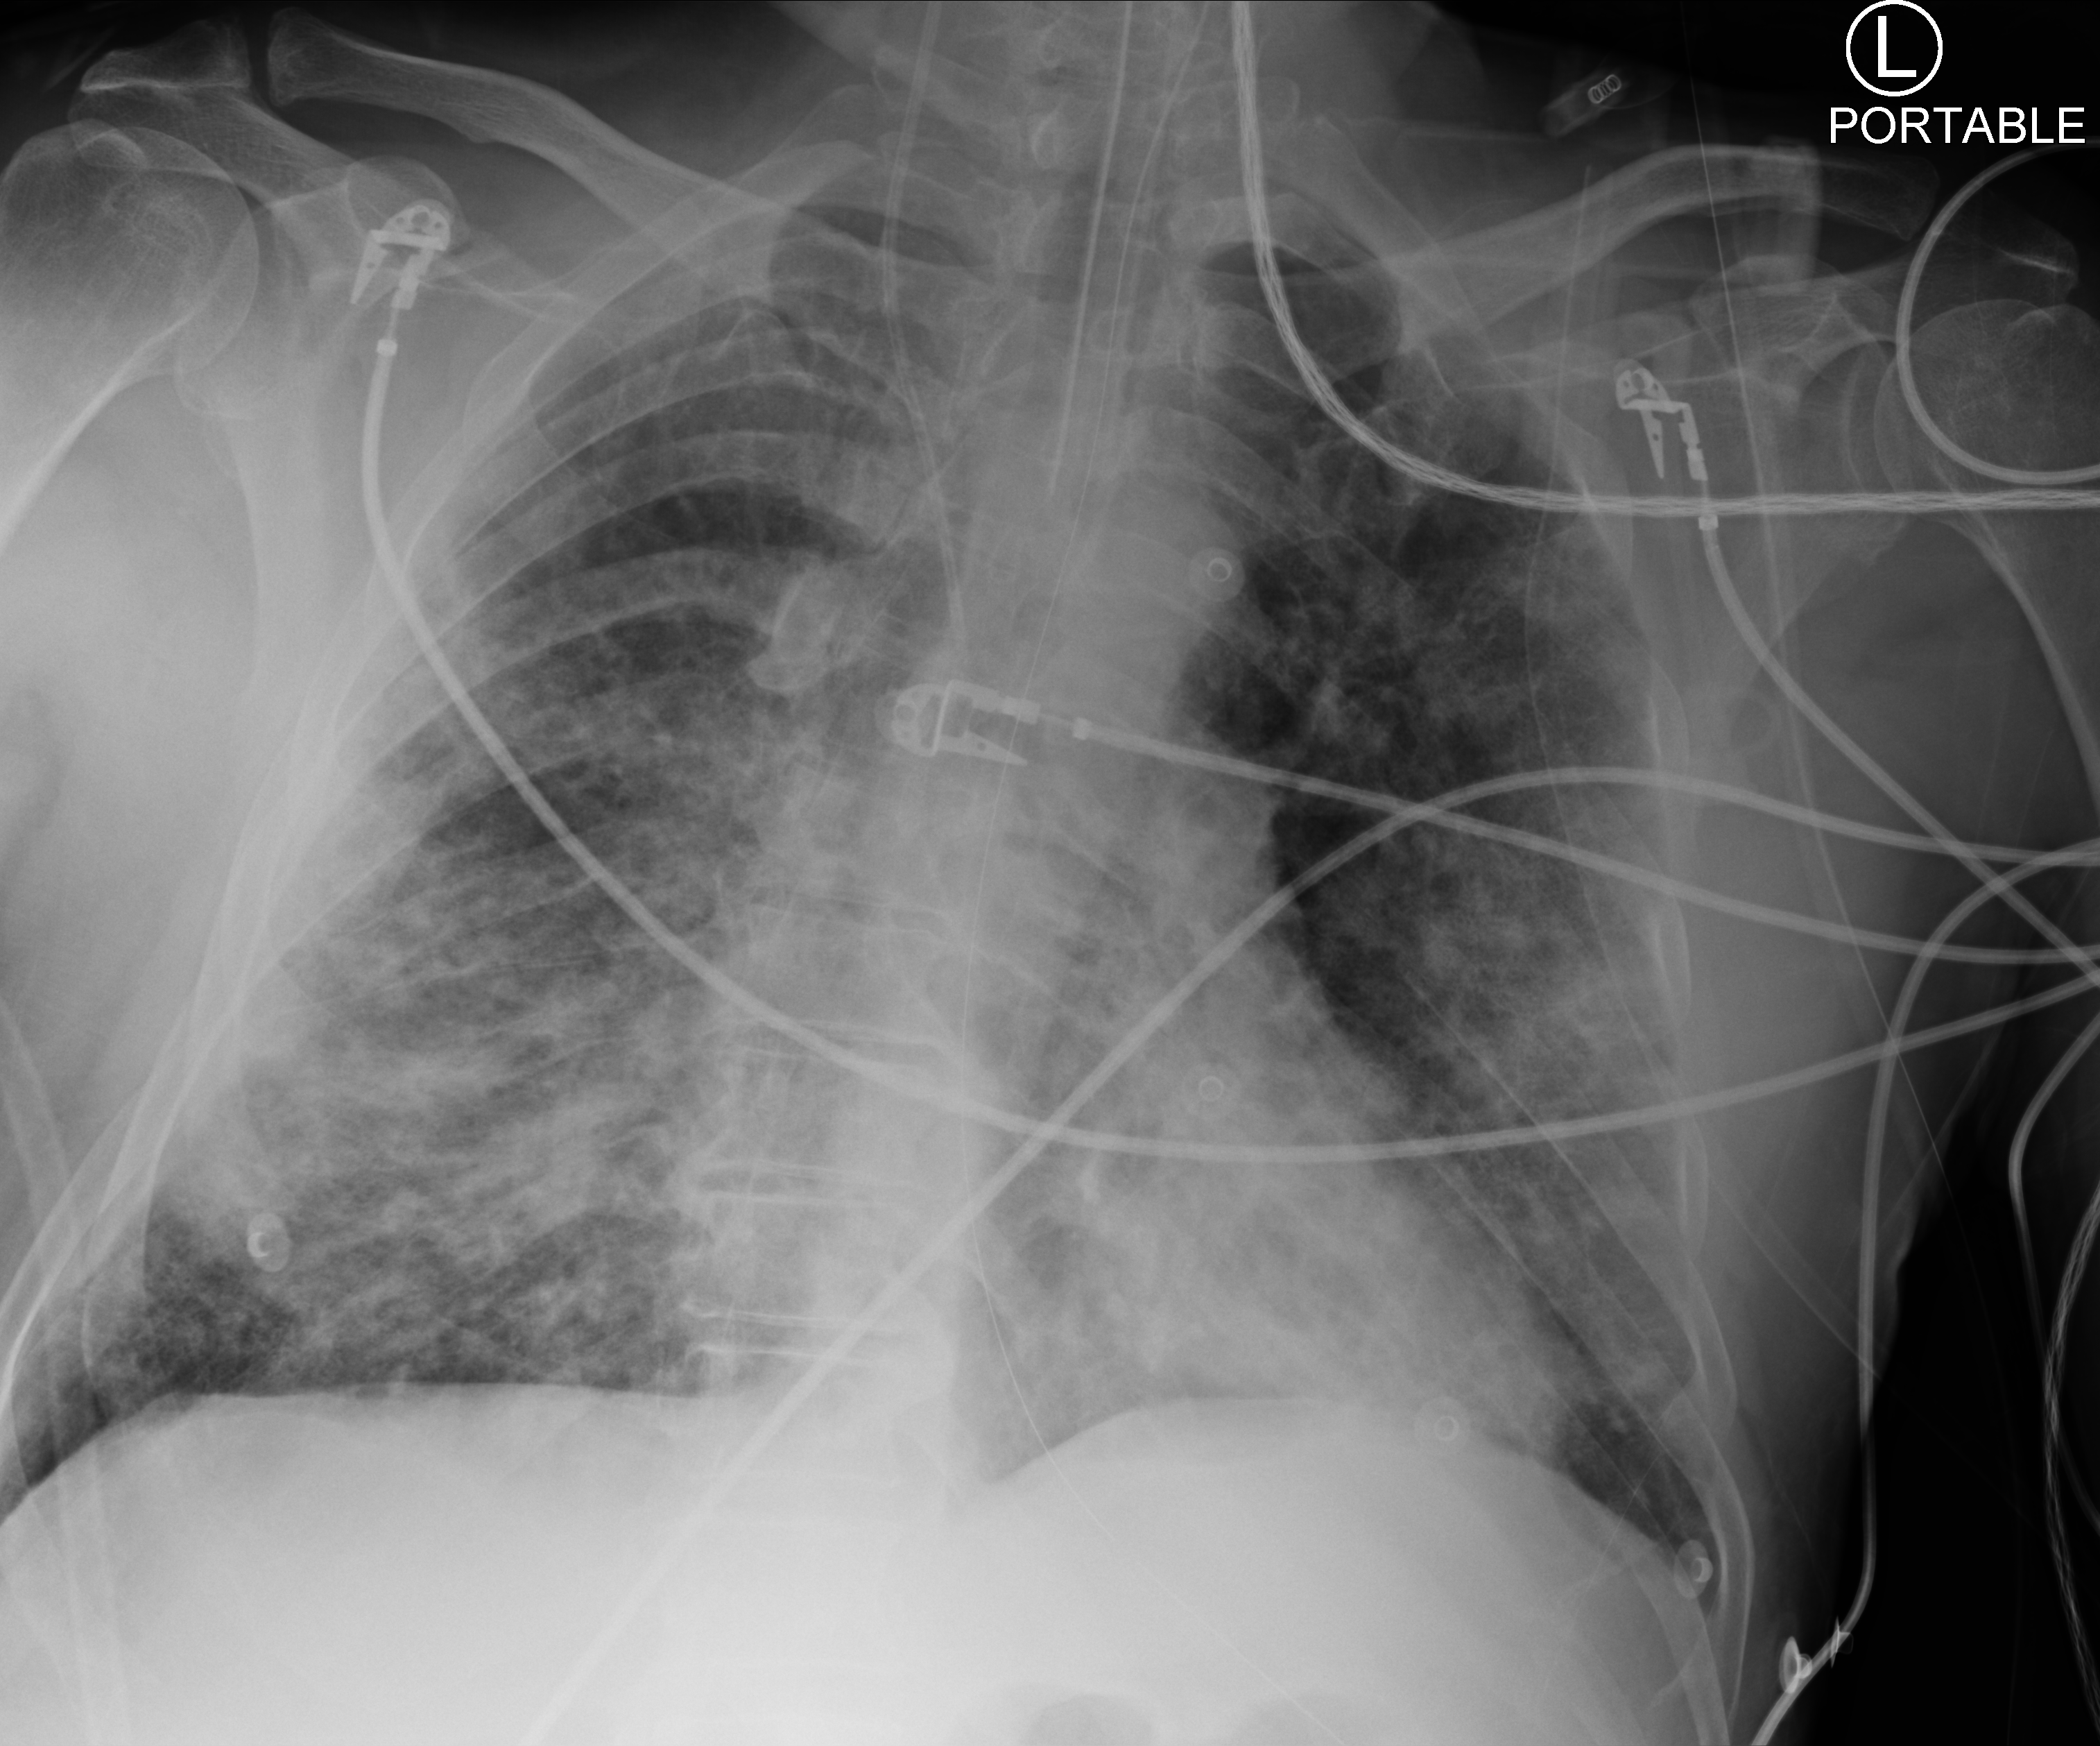
Portable chest radiograph; anteroposterior (AP) projection. Patient hospitalised with COVID-19; male, aged 60–74 years.
Hospital-stay facts (about this admission, not read from this image; timing relative to this image not recorded):
- chronic kidney disease (admission record): no
- hypertension (admission record): yes